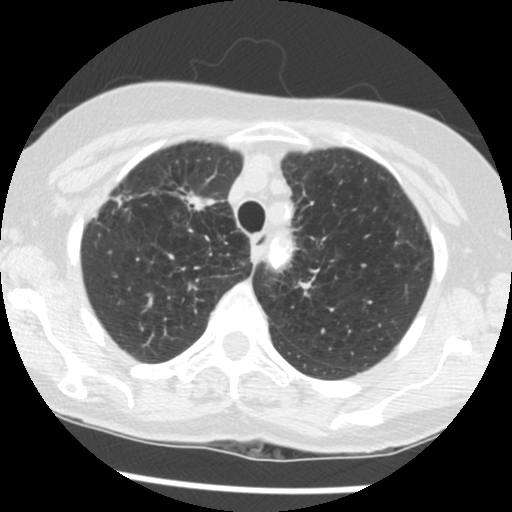
Axial slice from a low-dose chest CT screening exam, second screening round (one year after baseline), lung window (W 1500 / L -600 HU), slice 26 of 124 in the series. Female participant, aged 70 years at enrolment.
Expert reader's lesion annotation, box from (x=157, y=171) to (x=225, y=226) px. Reader record for this screening exam (exam-level; its link to the box is not recorded): non-calcified nodule or mass ≥4 mm, right upper lobe, 11 × 7 mm, spiculated (stellate) margins, soft tissue attenuation, pre-existing on the prior screen: yes; interval growth: yes. Official screen result: positive, other. Later outcome: lung cancer diagnosed 248 days after this screen — non-small cell carcinoma, right upper lobe, stage IV (AJCC 6th edition), 30 mm at pathology.